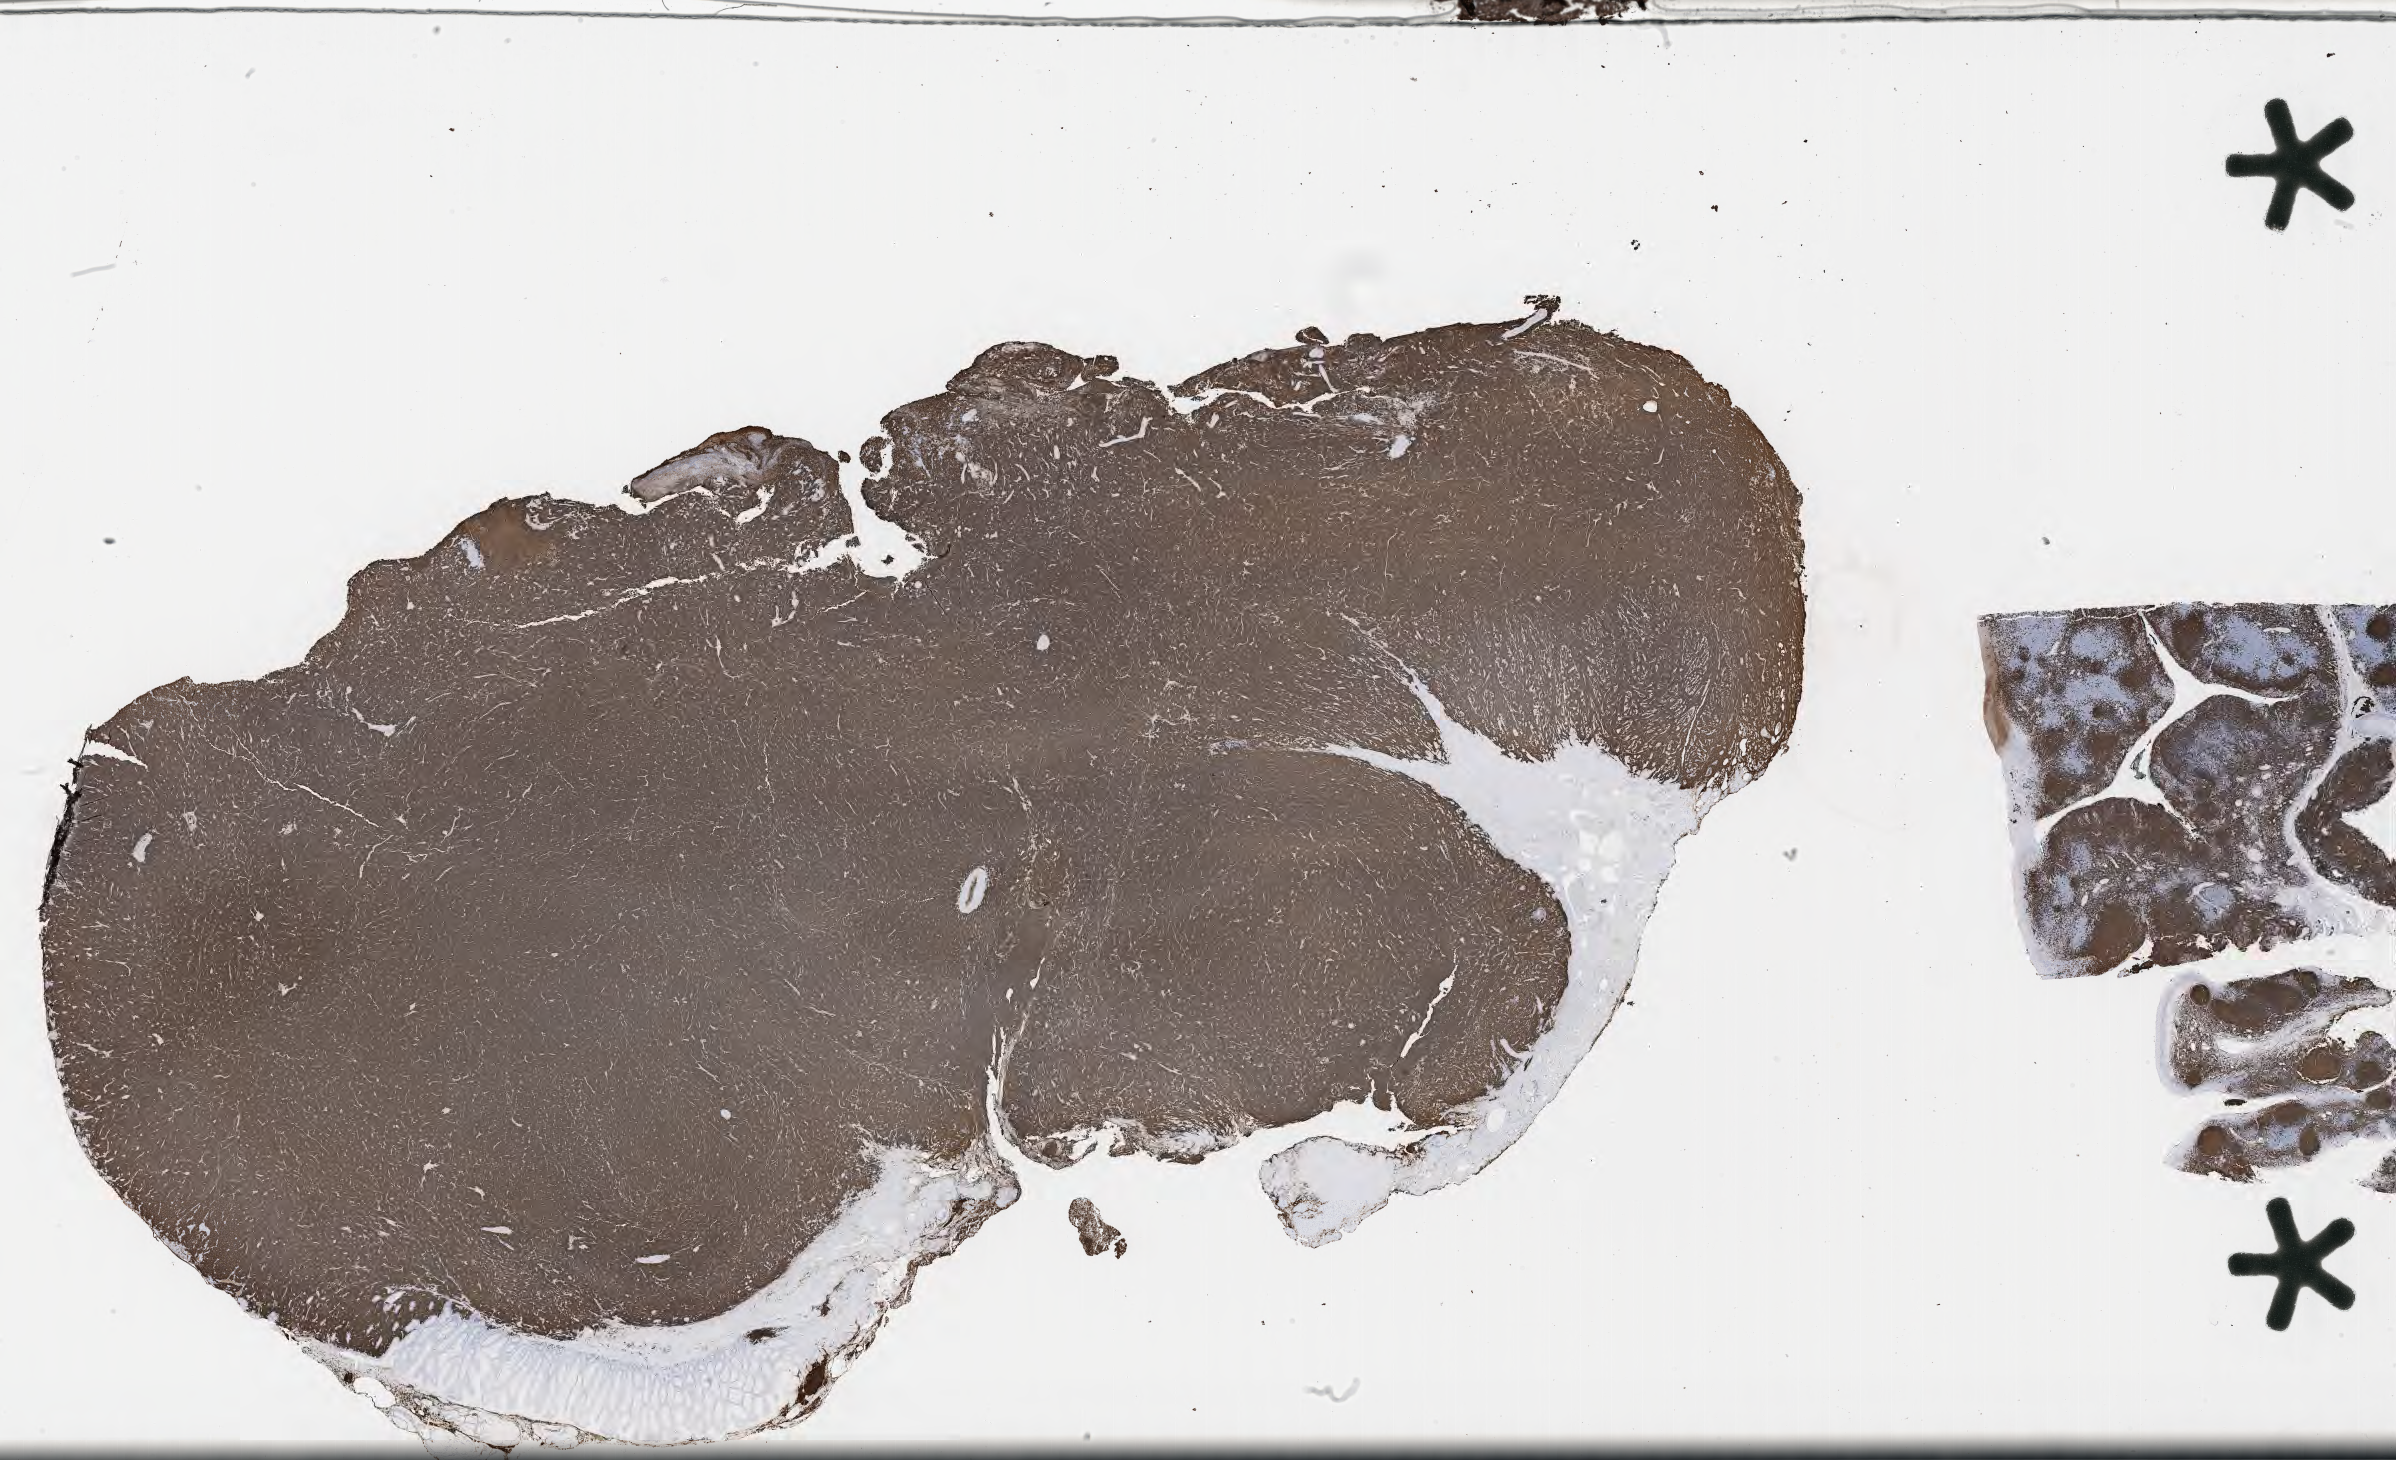
Whole-slide image, immunohistochemical stain for CD20, a low-resolution overview of the entire scanned area, about 38.7 x 23.6 mm. Tumor tissue. Patient female; aged 29.
Histologic diagnosis: Burkitt lymphoma, NOS.